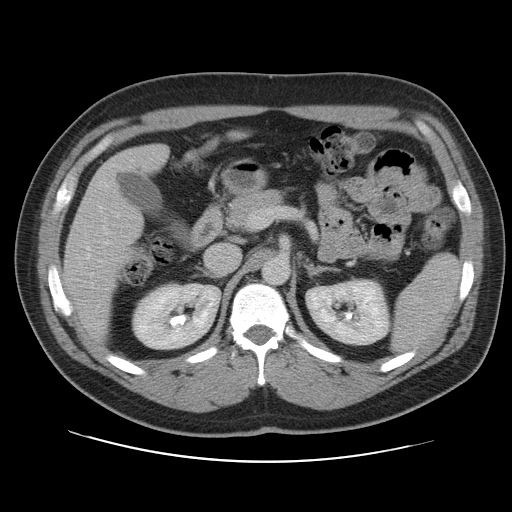
Contrast-enhanced abdominal CT, one axial slice; position 61 of 109 along the scan axis; soft-tissue window (W 400 / L 40 HU); 5 mm slice thickness; 512 × 512 image matrix, field of view 402 × 402 mm. Male patient, age 35 years. Case-level facts recorded for this patient, not image findings: diagnosis: colorectal cancer liver metastases, imaged before liver resection; multiple liver metastases: yes; largest metastasis: 2.8 cm; disease in both lobes: yes.
Structures marked on this image (expert manual segmentation):
- liver: bounding box [x1, y1, x2, y2] px = [65, 145, 167, 341]
- planned liver remnant (the part of the liver to remain after resection): [65, 145, 167, 341]